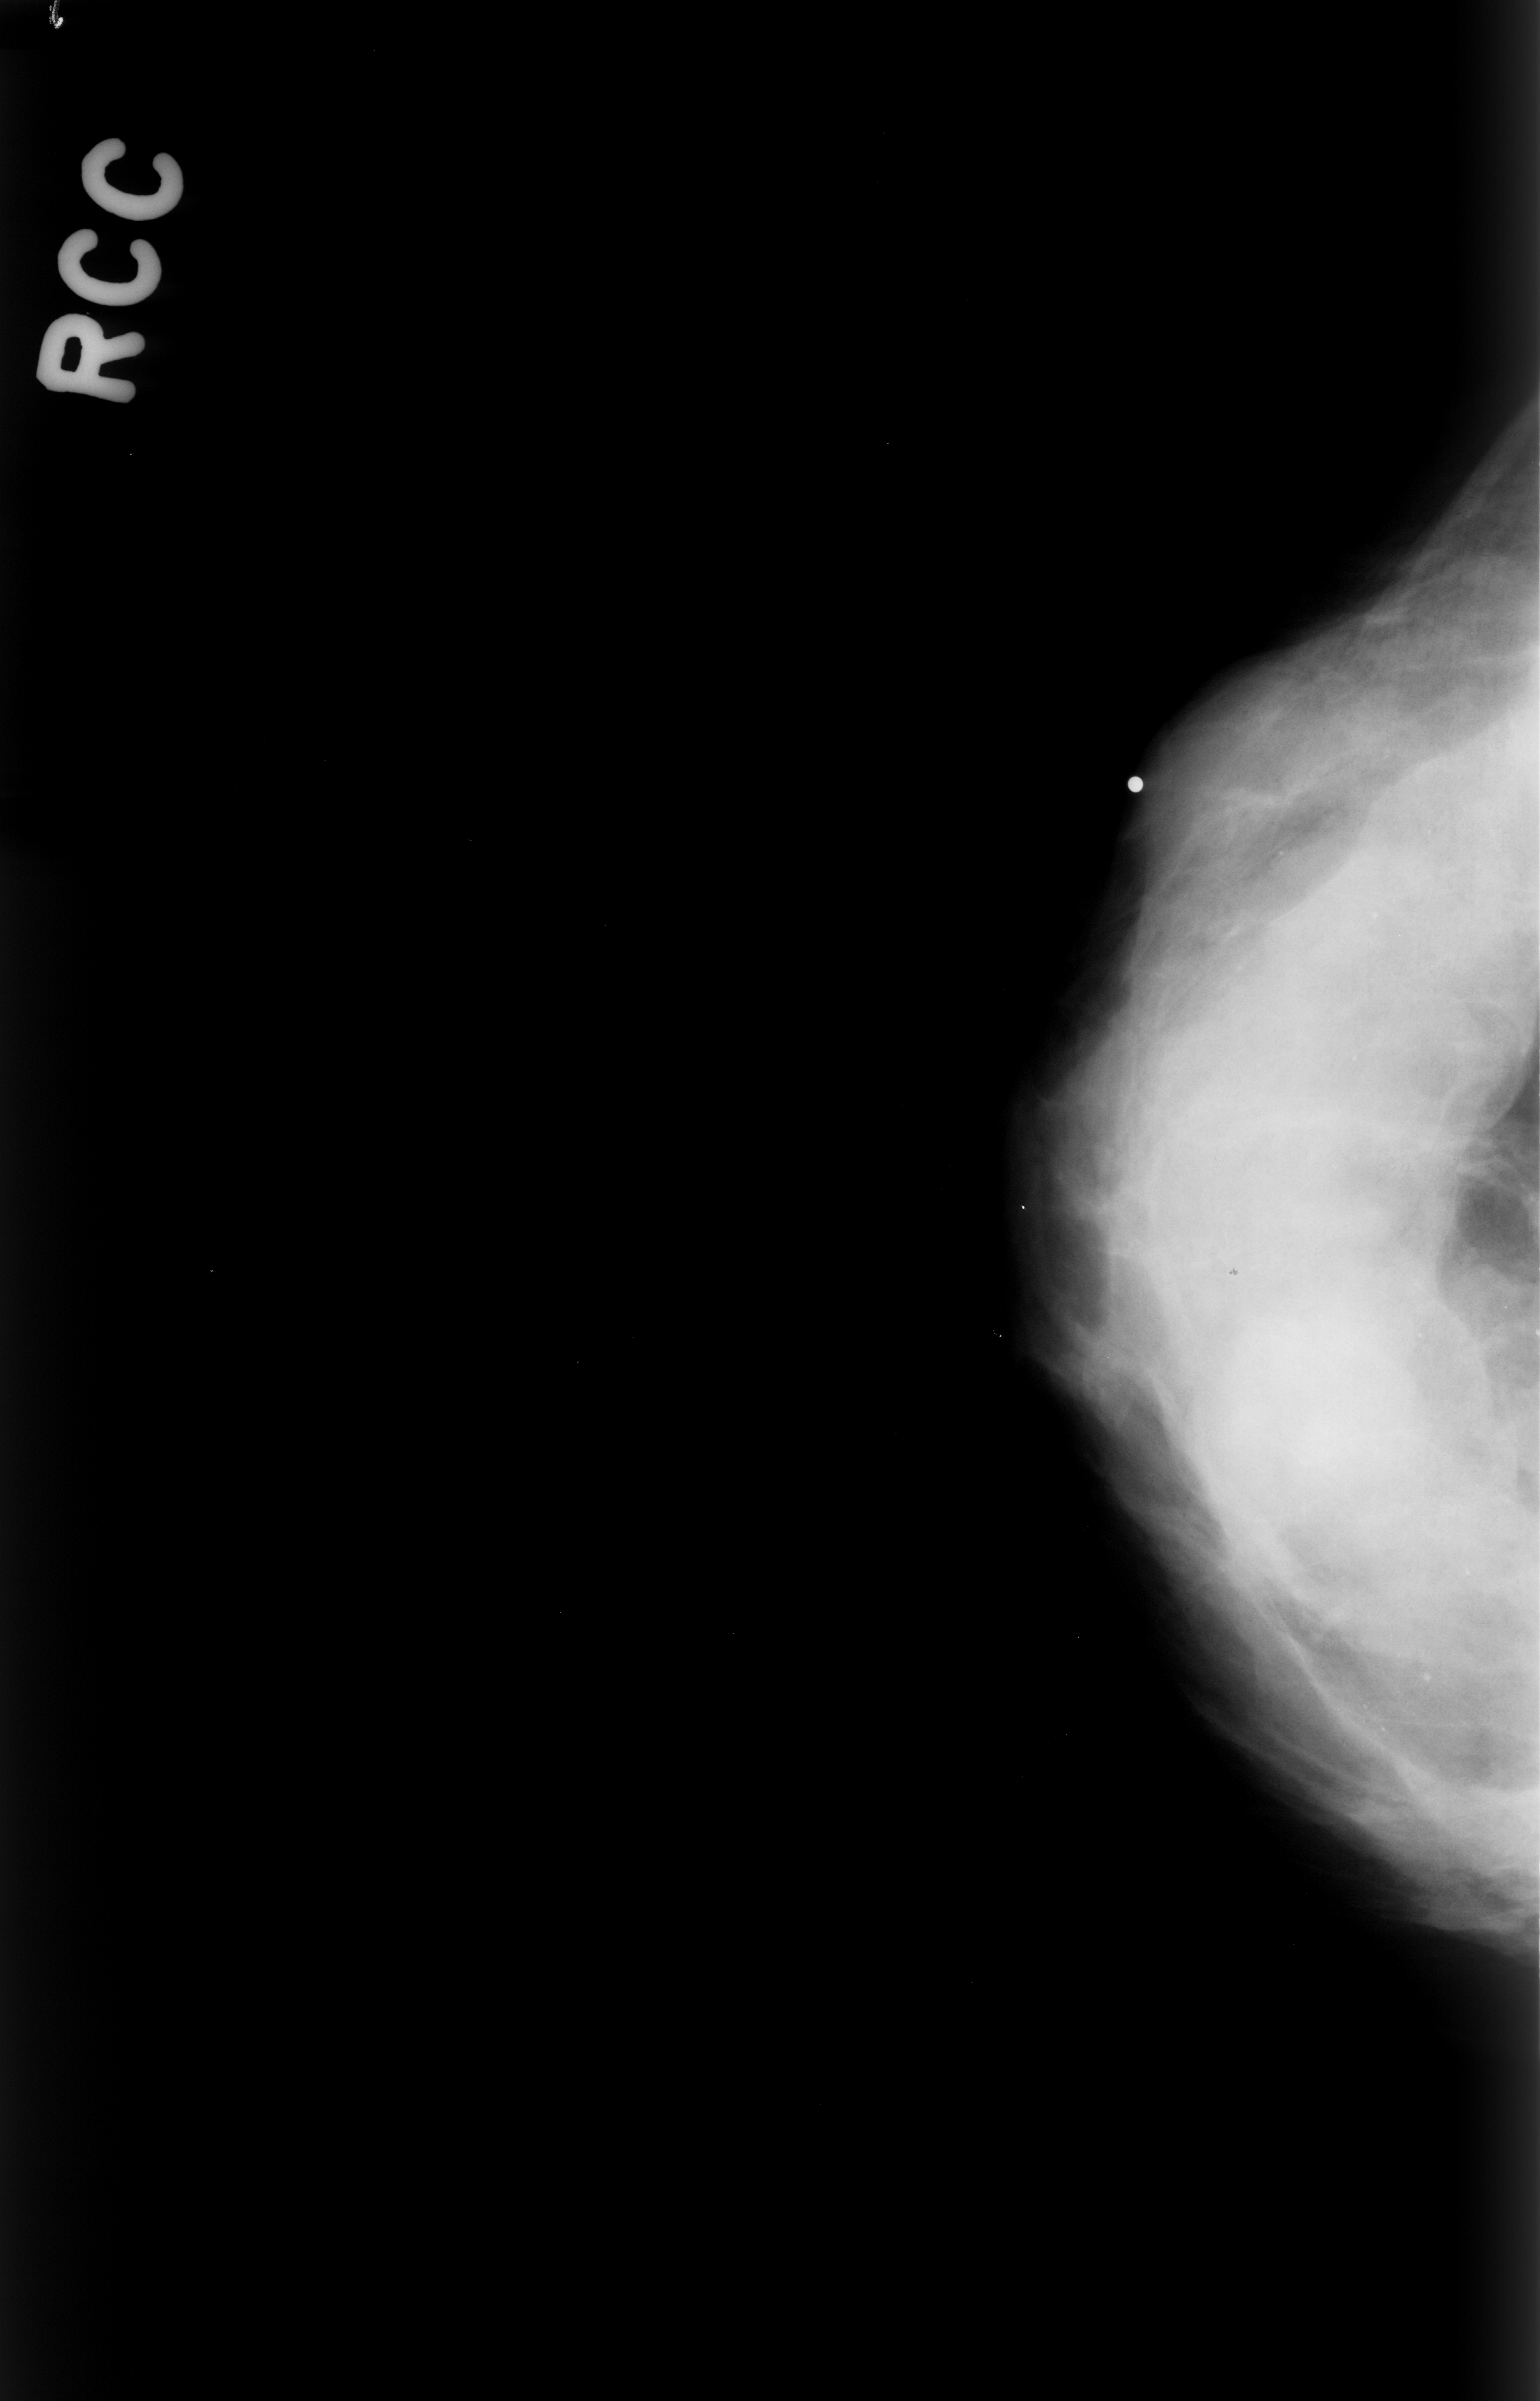
Digitized screen-film mammogram, right breast, craniocaudal (CC) view, breast composition: extremely dense (BI-RADS density category 4 of 4).
Calcifications, morphology punctate, distribution diffusely scattered; BI-RADS assessment category 2; subtlety rating 4 on a 1 (subtle) to 5 (obvious) scale; pathology result (as recorded, not read from the image): benign.